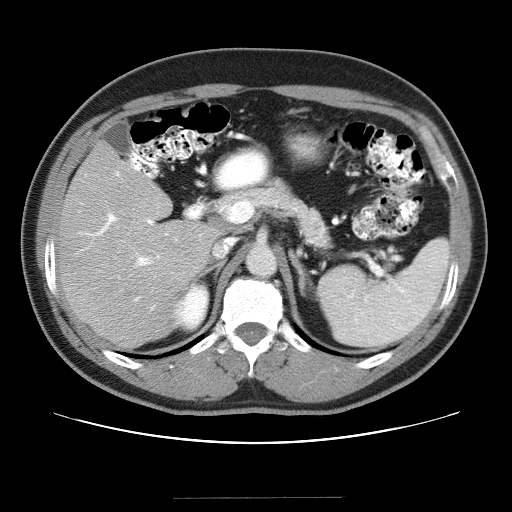
Contrast-enhanced abdominal CT (liver protocol), one axial slice; slice 18 of 40 in the series (ordered by position); reconstruction kernel STANDARD; 120 kVp; soft-tissue window (W 400 / L 40 HU); 5 mm slice thickness; 512 × 512 image matrix, field of view 380 × 380 mm. From the clinical record (not read from this slice): diagnosis: hepatocellular carcinoma (patient treated with transarterial chemoembolisation; whether this scan precedes or follows treatment is not stated here); TNM stage (as recorded): Stage-IVA; Child-Pugh class: B; tumour nodularity: multinodular.
Outlined on this slice (semi-automatic segmentation, software-assisted and operator-edited):
- liver parenchyma outside the tumour (the mass and vessels are separate outlines, so this box may not span the whole liver): bounding box <56,140,228,348> (left, top, right, bottom; pixels)
- liver vessels: <79,171,201,311>